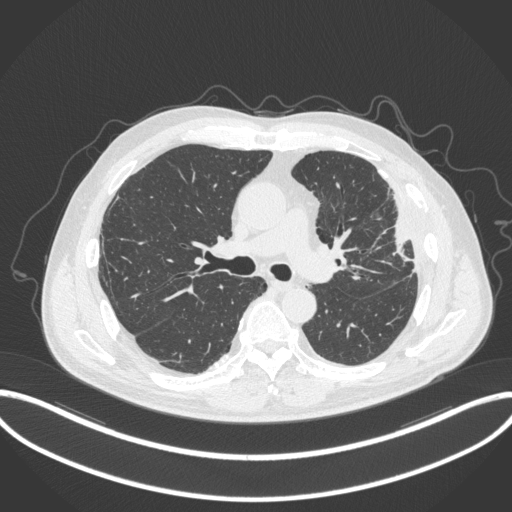
Chest CT, one axial slice; reconstruction kernel B31f; 120 kVp; lung window (W 1500 / L -600 HU); 1 mm slice thickness; 512 × 512 image matrix, field of view 415 × 415 mm. Patient: male, 64 years. From the clinical record (not read from this slice): clinical TNM (as recorded): T4 N1 M0; histopathological grade: G3.
Annotated regions visible in this slice (rectangle marked by the reading radiologist):
- lung tumour (recorded histology: adenocarcinoma): box from (x=383, y=194) to (x=414, y=271) px